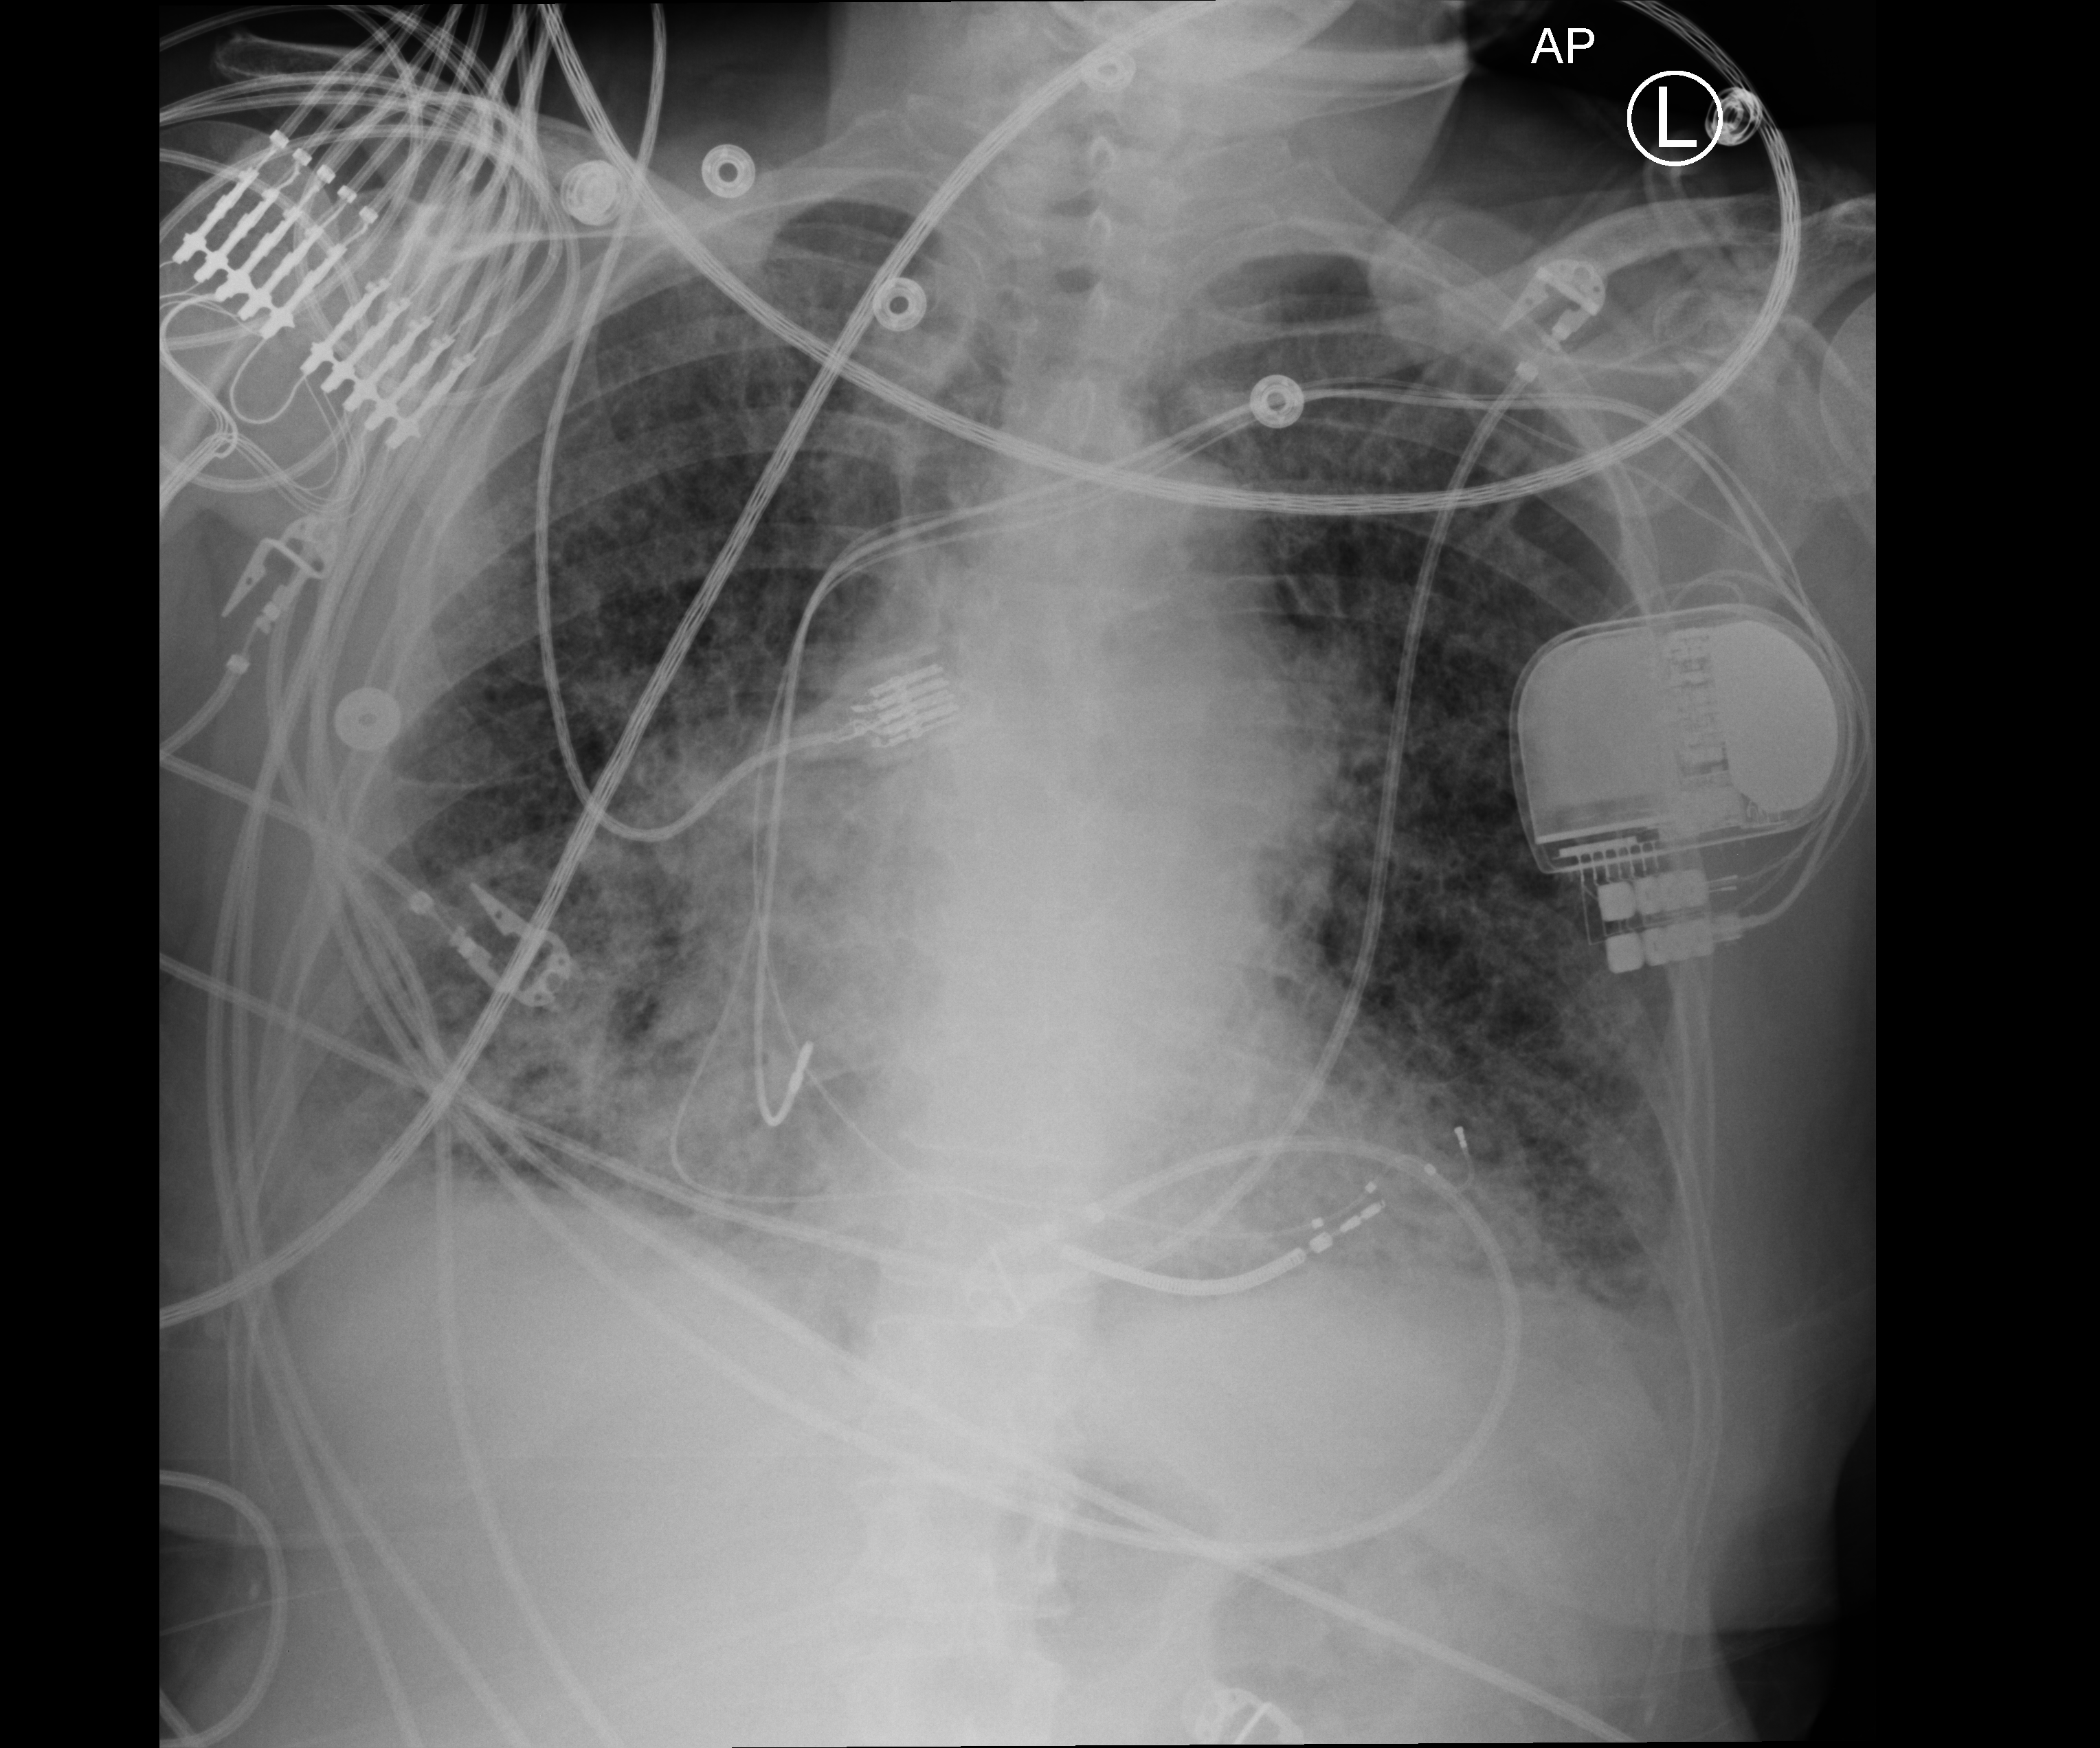
Chest X-ray (portable); anteroposterior (AP) projection. Patient hospitalised with COVID-19; female, aged 60–74 years.
From the hospital-stay record, not from the radiograph (when in the stay this image was taken is not recorded):
- admitted to intensive care during this hospital stay: yes